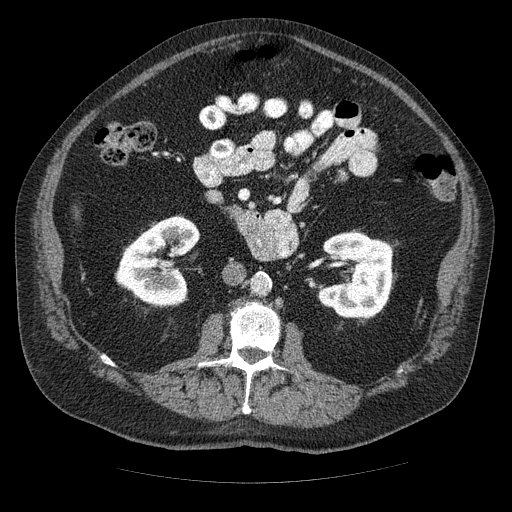
Contrast-enhanced abdominal CT (liver protocol), one axial slice. Slice 5 of 85 in the series (ordered by position). Reconstruction kernel STANDARD. Soft-tissue window (W 400 / L 40 HU). 2.5 mm slice thickness. 512 × 512 image matrix, field of view 420 × 420 mm. Case-level facts recorded for this patient, not image findings: diagnosis: hepatocellular carcinoma (patient treated with transarterial chemoembolisation; whether this scan precedes or follows treatment is not stated here); TNM stage (as recorded): Stage-IIIA.
Structures marked on this image (semi-automatically segmented with operator editing):
- liver parenchyma outside the tumour (the mass and vessels are separate outlines, so this box may not span the whole liver): box from (x=74, y=209) to (x=78, y=217) px